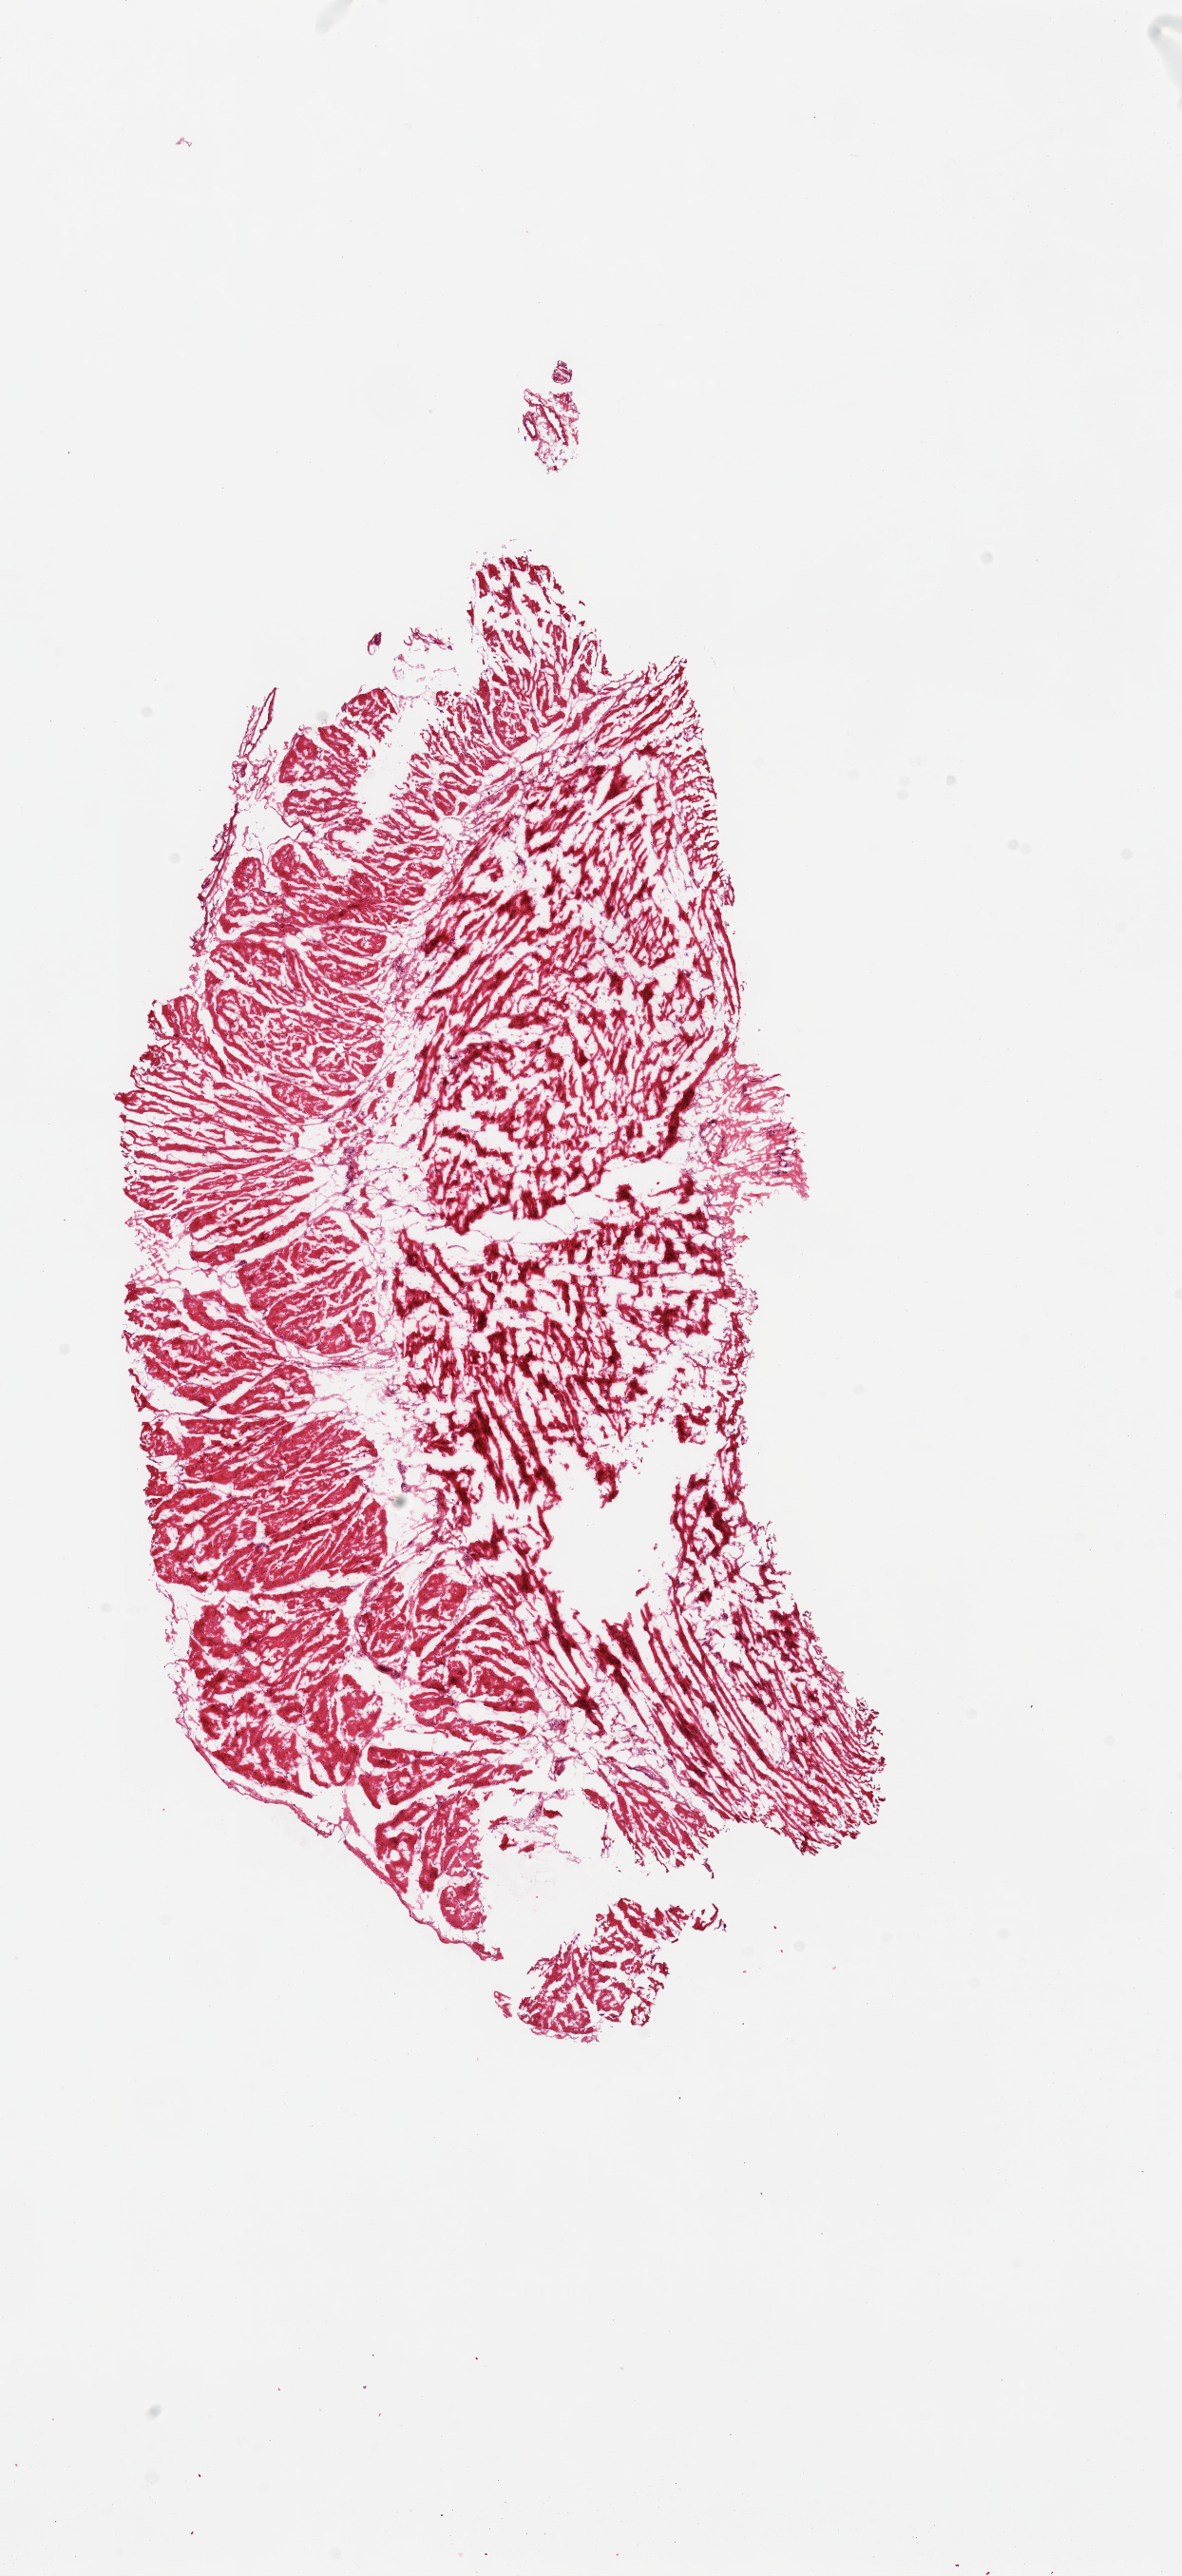
Haematoxylin and eosin whole-slide image, low-resolution overview of the scanned area, about 9.8 x 21.4 mm (acquisition: 20x scan). Donor sex: female.
* specimen: frozen section; sampled site (target tissue): esophageal muscle; tissue donor sample